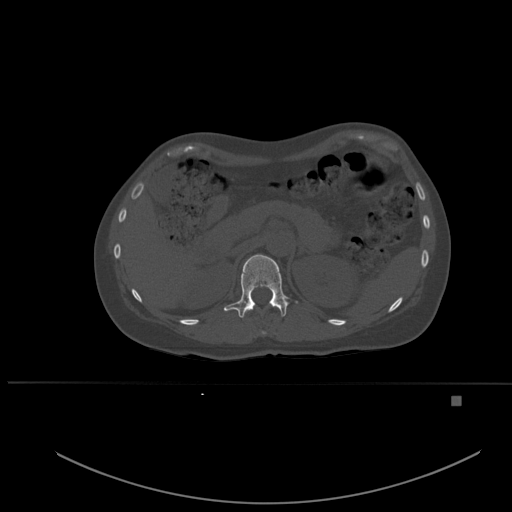
CT including the spine, one axial slice; slice 257 of 651 in the series (ordered by position); bone window (W 1800 / L 400 HU); 1.5 mm slice thickness; 512 × 512 image matrix, field of view 443 × 443 mm. Female patient, age 49 years. Case-level facts recorded for this patient, not image findings: primary cancer: breast; vertebrae with lytic lesions (as recorded): L3, T12, L4.
Structures marked on this image (semi-automatic segmentation, software-assisted and operator-edited):
- T11 vertebra: box from (x=262, y=331) to (x=266, y=334) px
- T12 vertebra: (x=223, y=254)–(x=298, y=318)